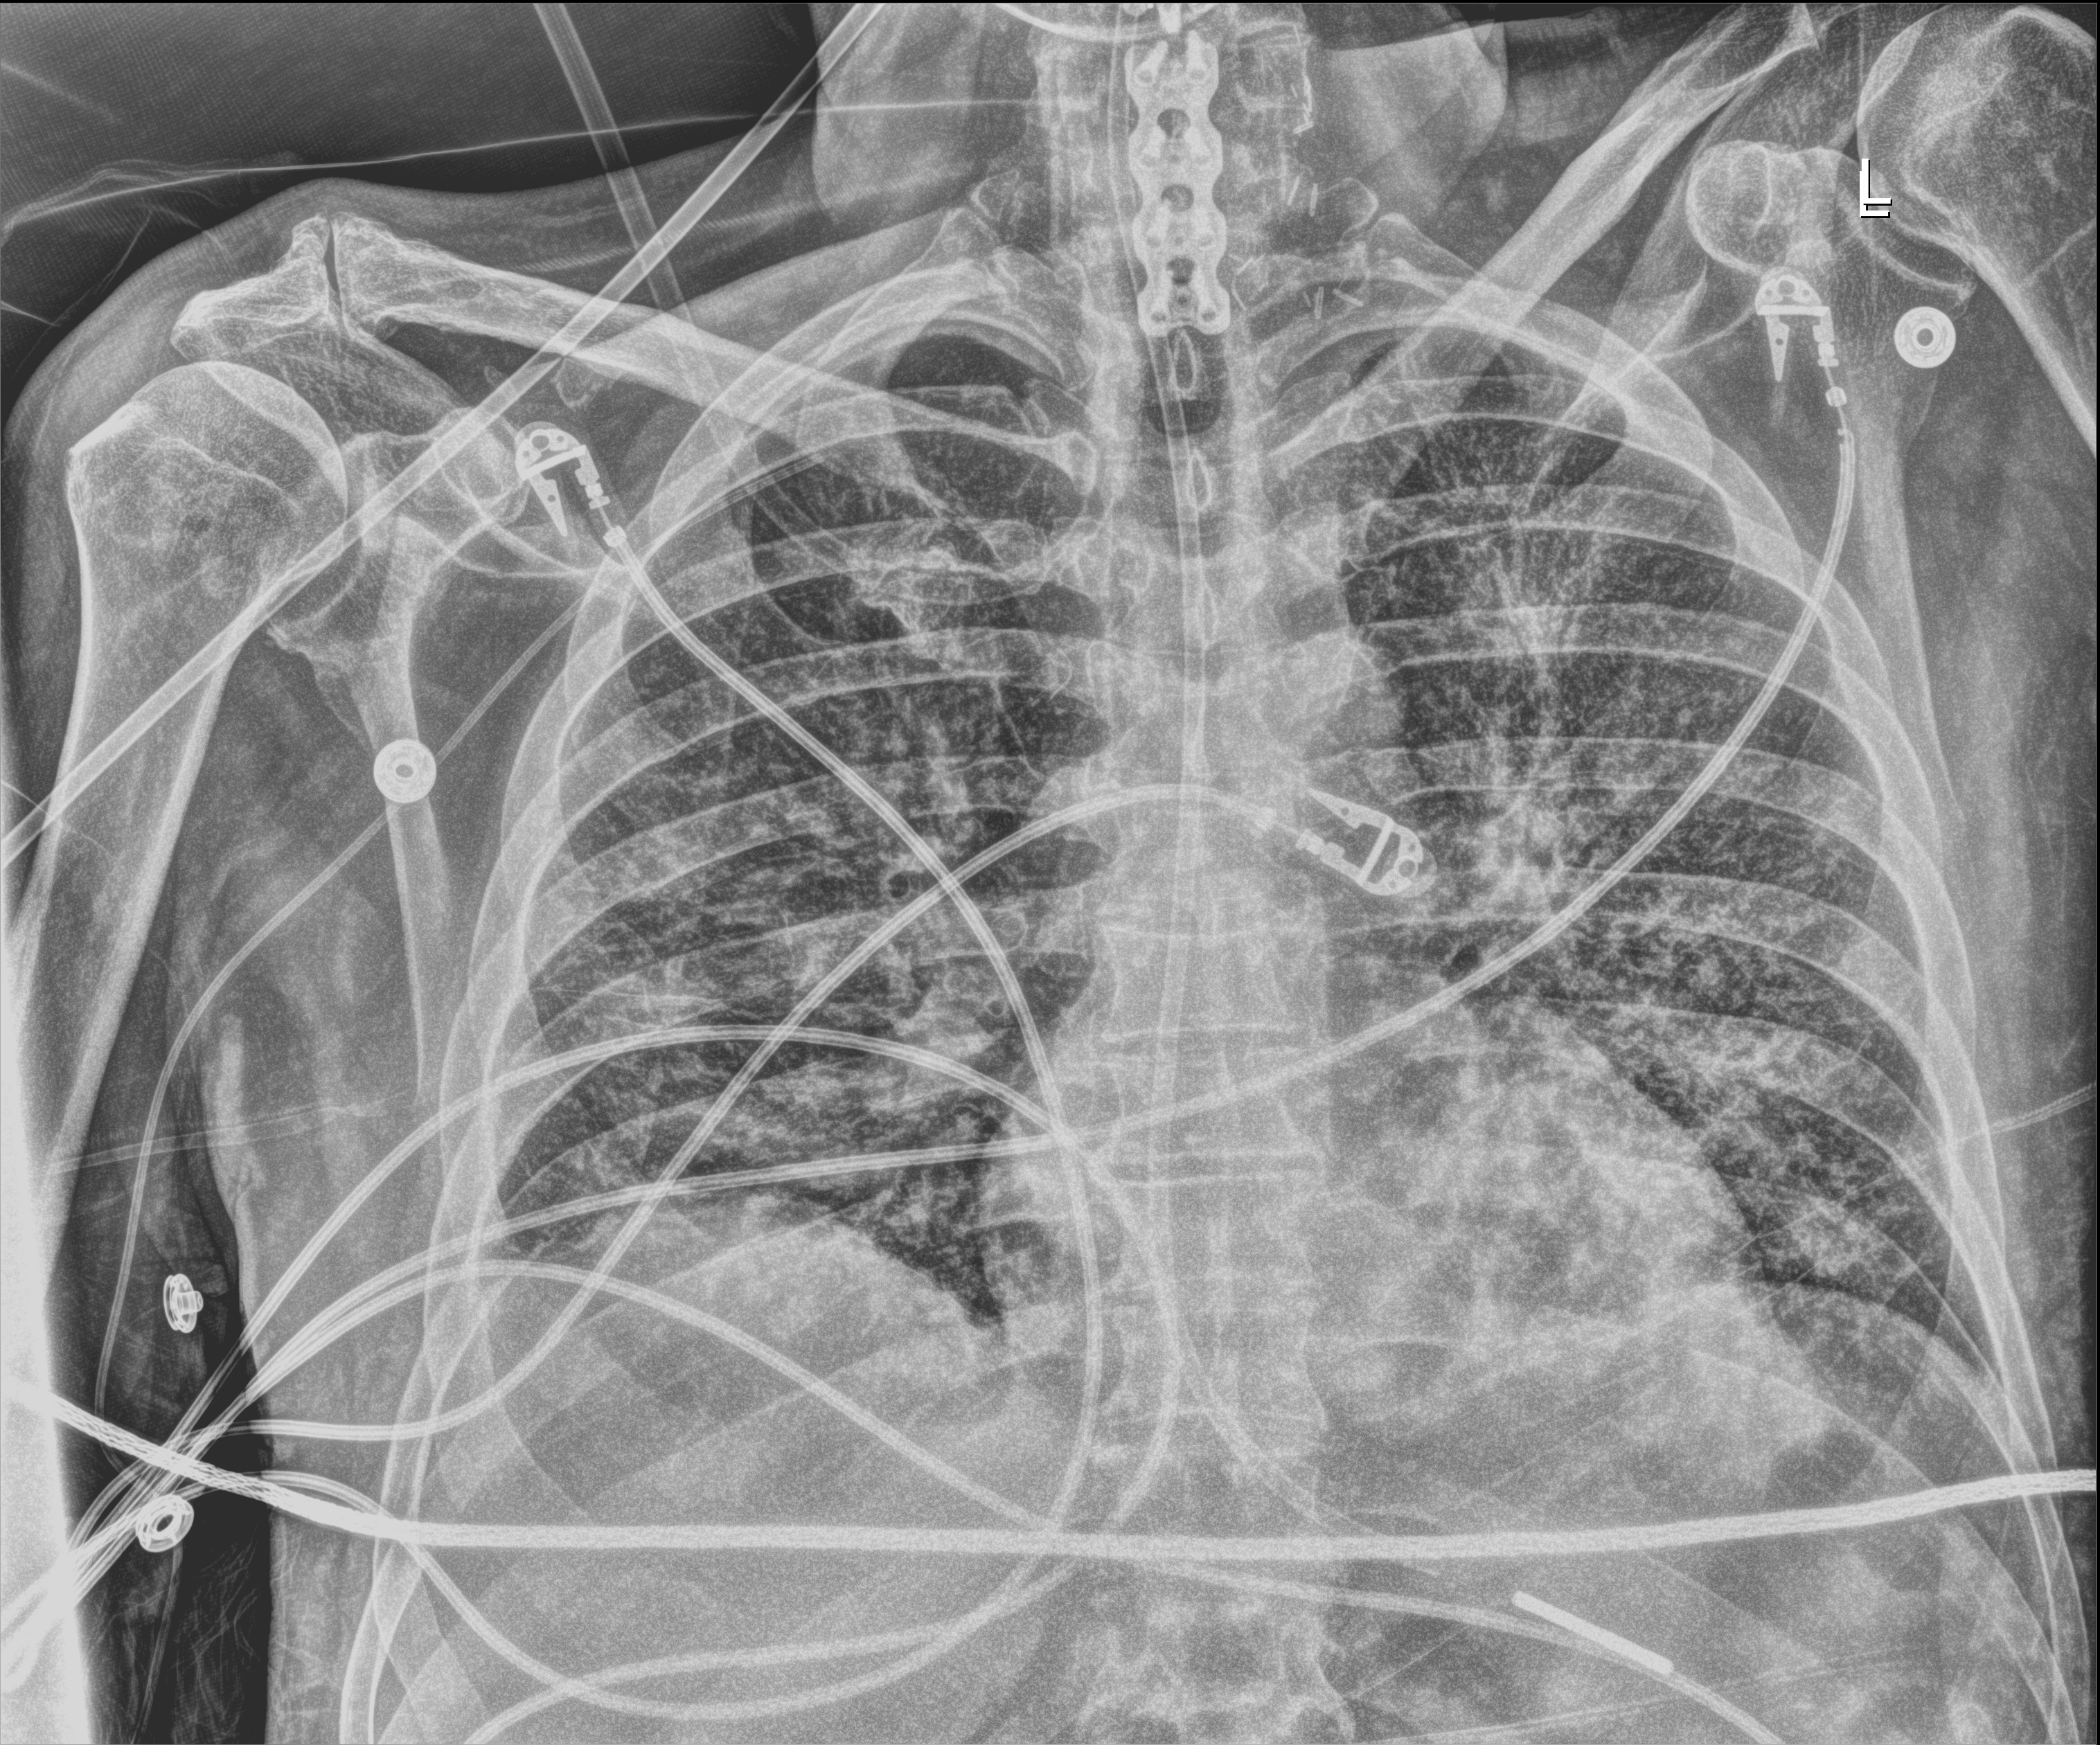
Portable chest radiograph. Male patient hospitalised with COVID-19, age 60–74 years.
Admission-level facts for this patient (not findings on this image; timing relative to this image not recorded): admitted to intensive care during this hospital stay: yes.